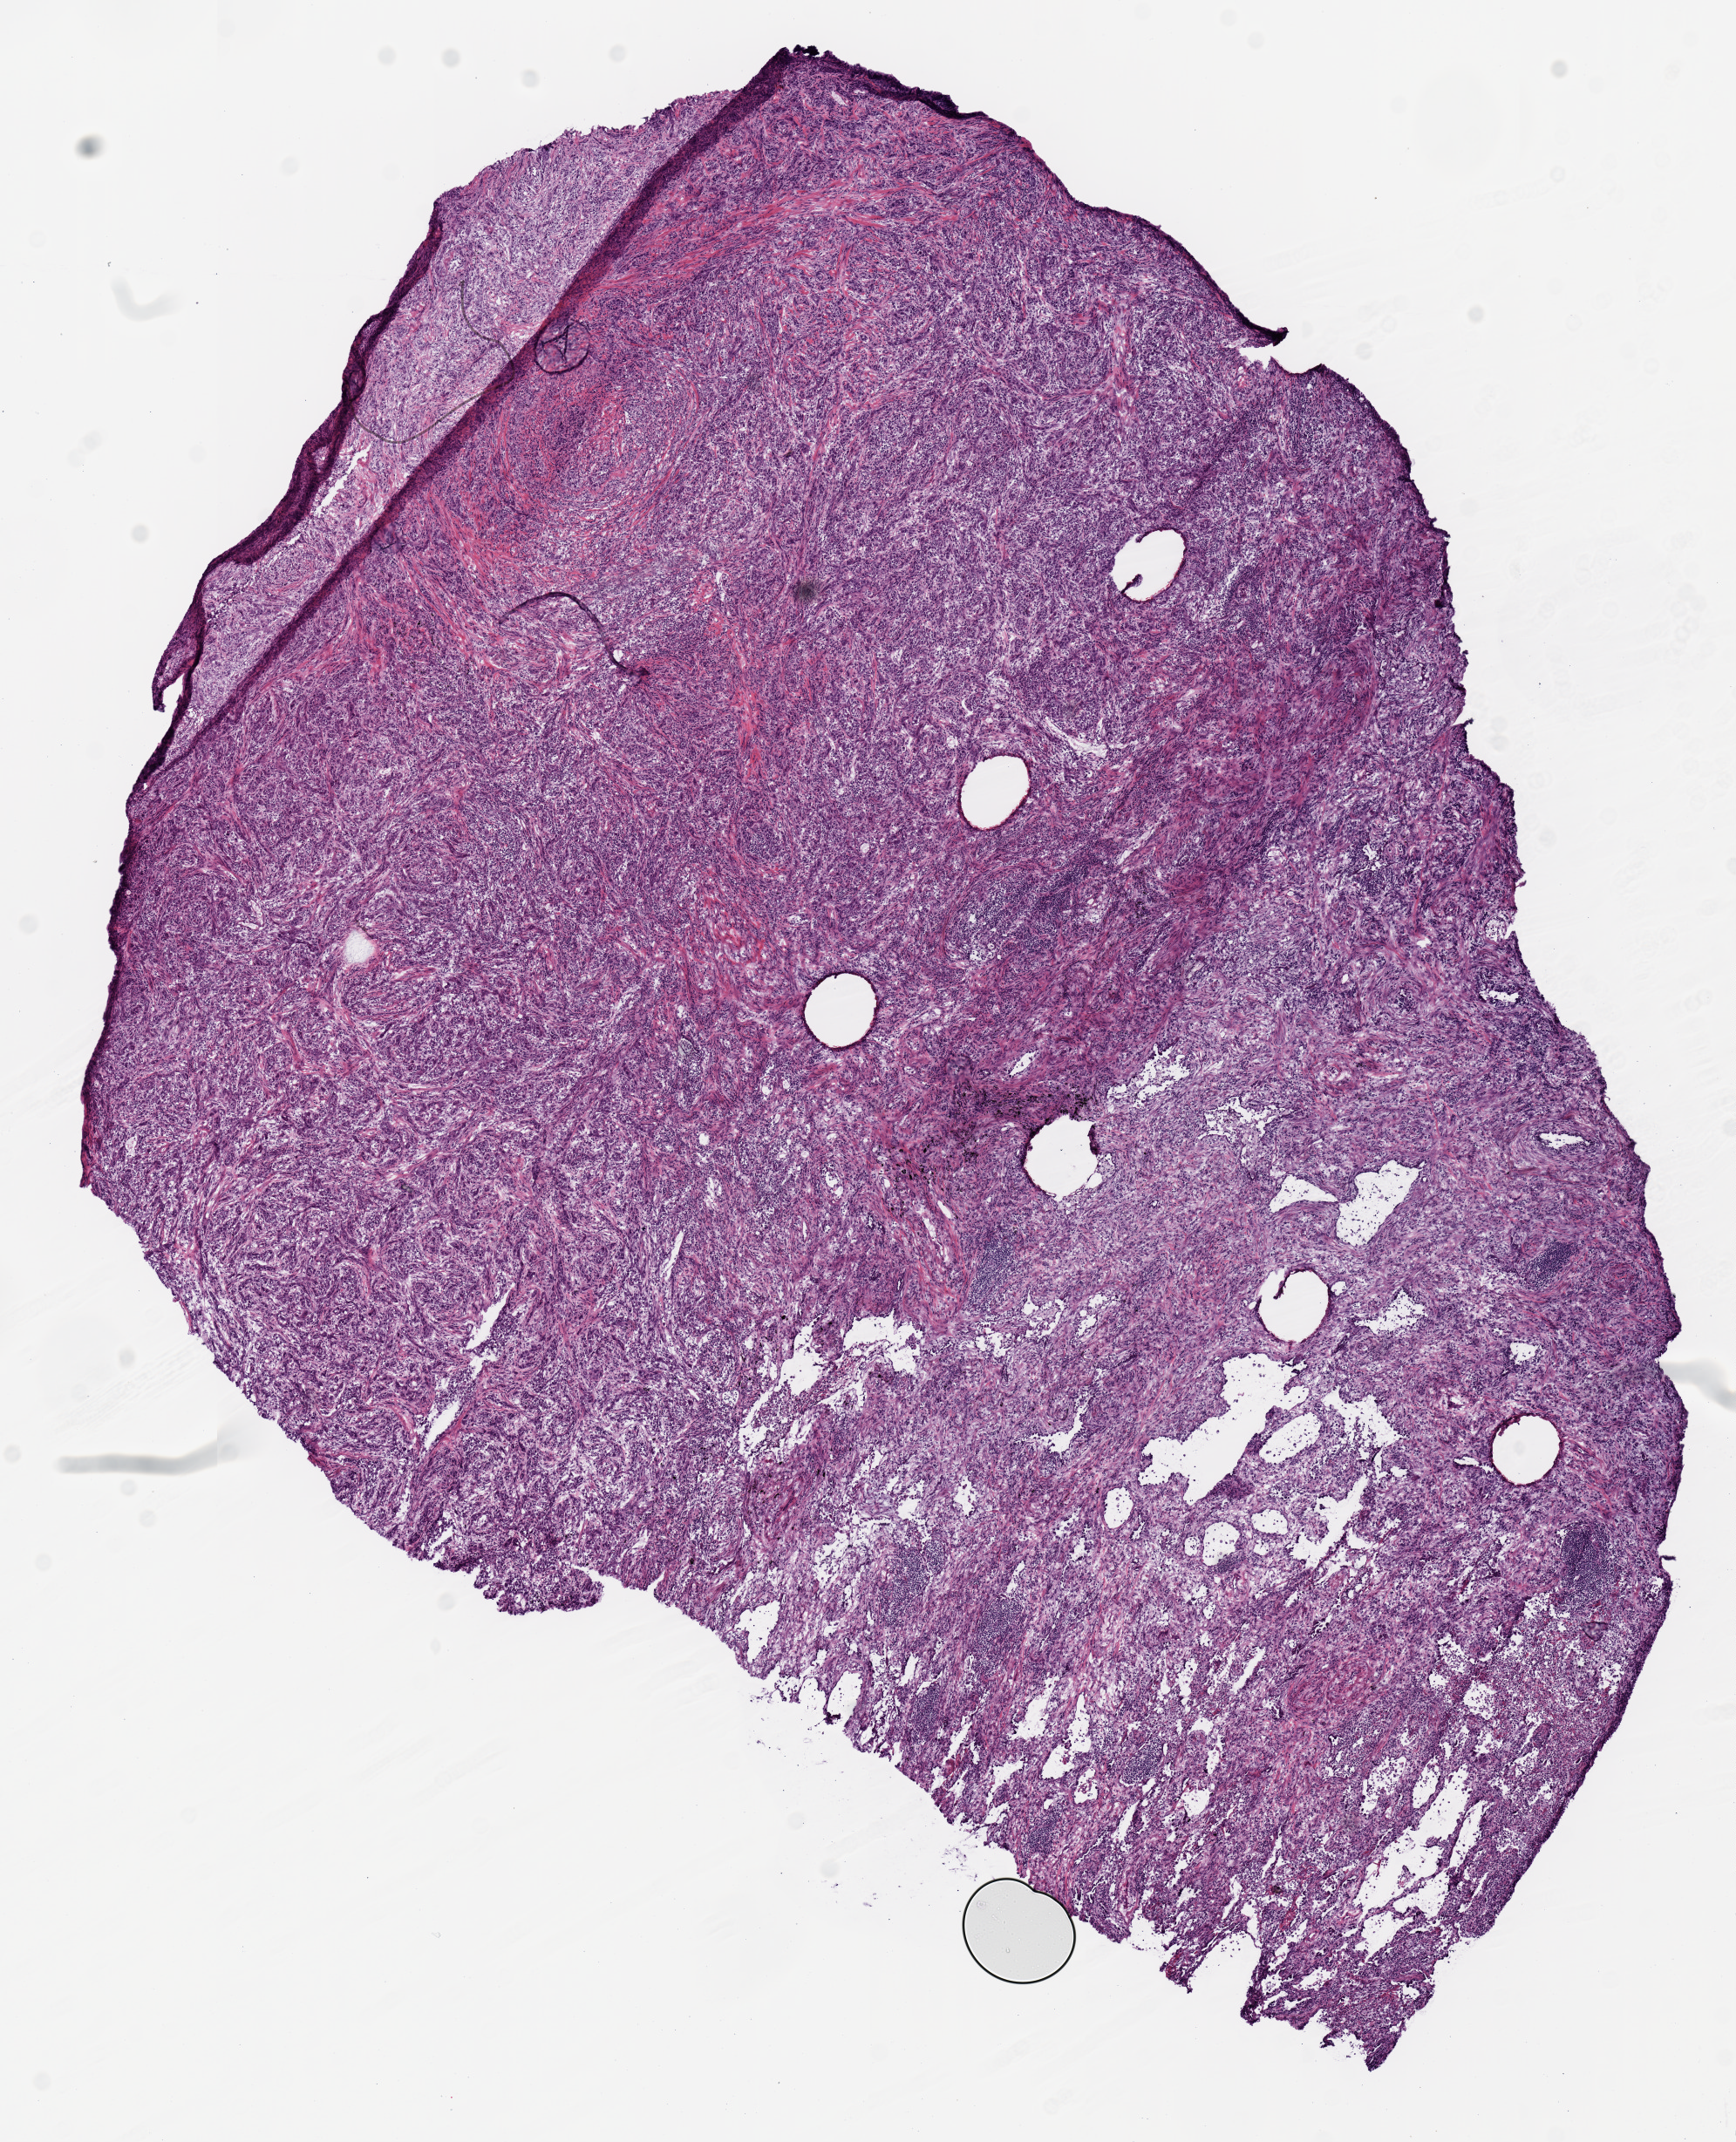
Digitized H&E tissue section (whole slide) — low-resolution overview of the scanned area, about 7.9 x 9.7 mm (acquisition: 20x scan); frozen section from the top of the tissue portion; primary tumour sample from the lung. Male patient; age at initial diagnosis 74 years. Slide review estimates, as recorded: tumour cells 90%, tumour nuclei 60%.
Histologic diagnosis: Squamous cell carcinoma, NOS (upper lobe, lung).